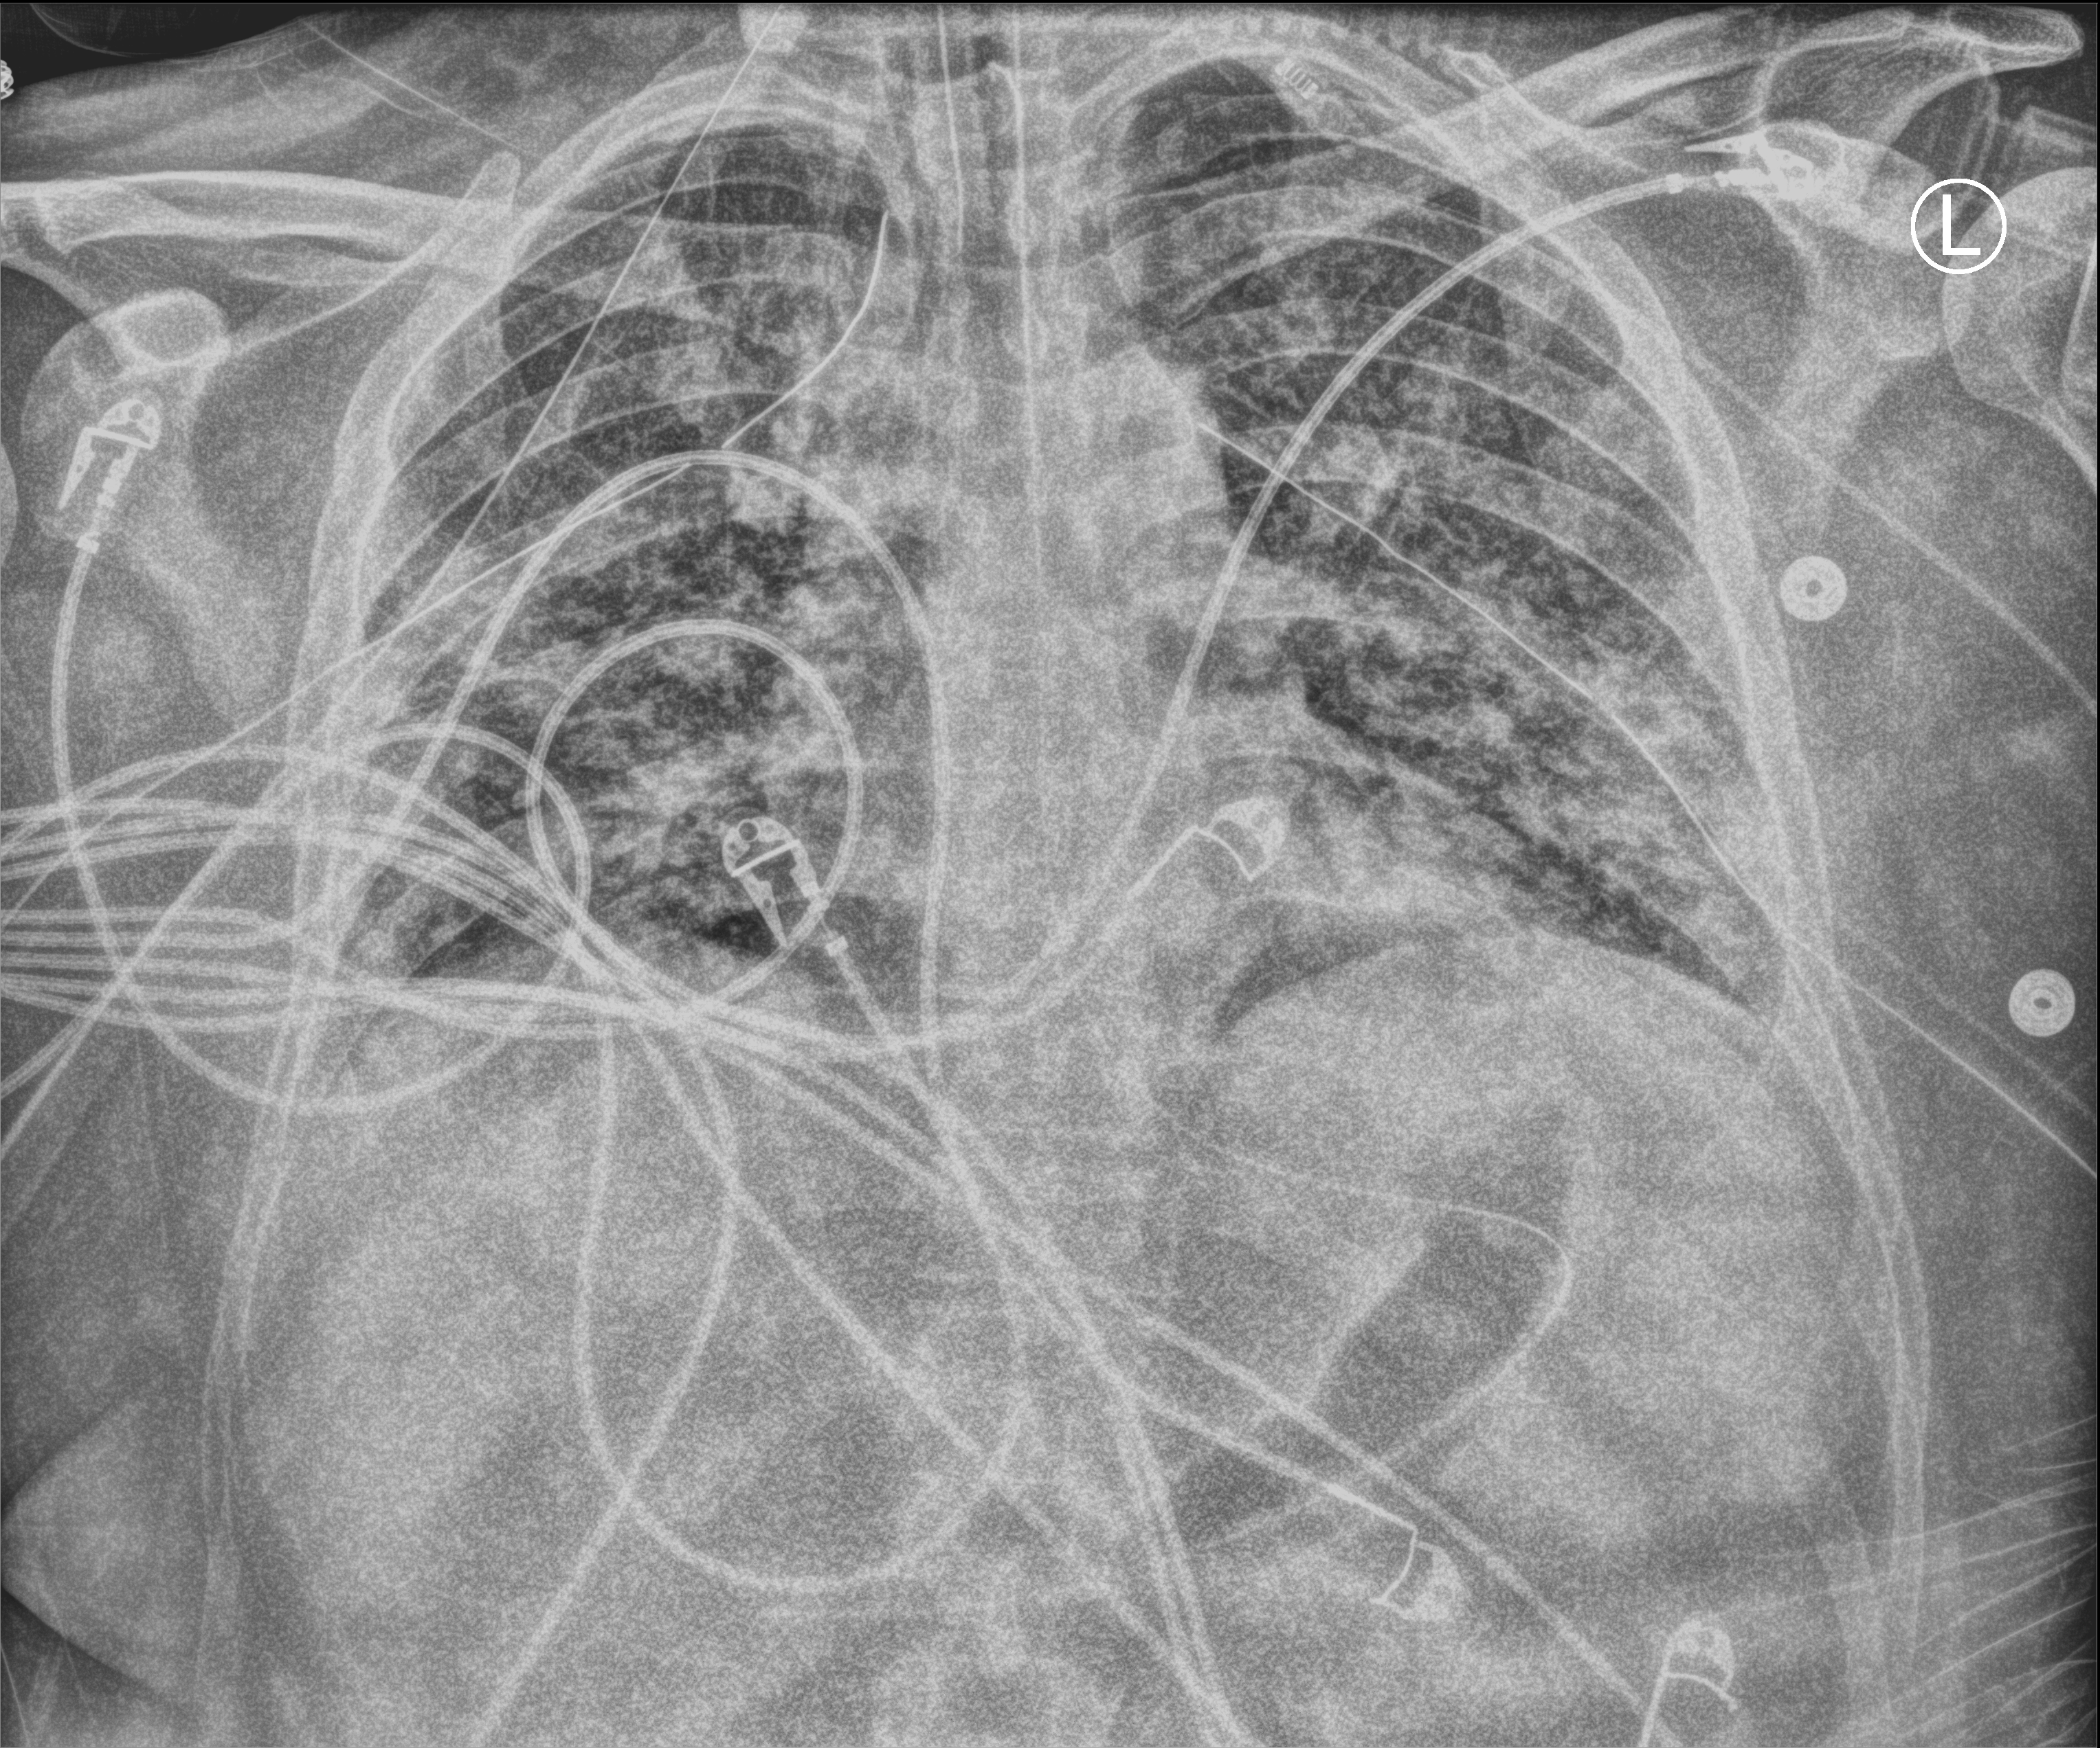
Chest X-ray (portable), anteroposterior (AP) projection. Patient hospitalised with COVID-19; male, aged 18–59 years.
From the hospital-stay record, not from the radiograph (when in the stay this image was taken is not recorded): length of hospital stay: 63 days; hypertension (admission record): yes; mechanically ventilated during this hospital stay: yes.